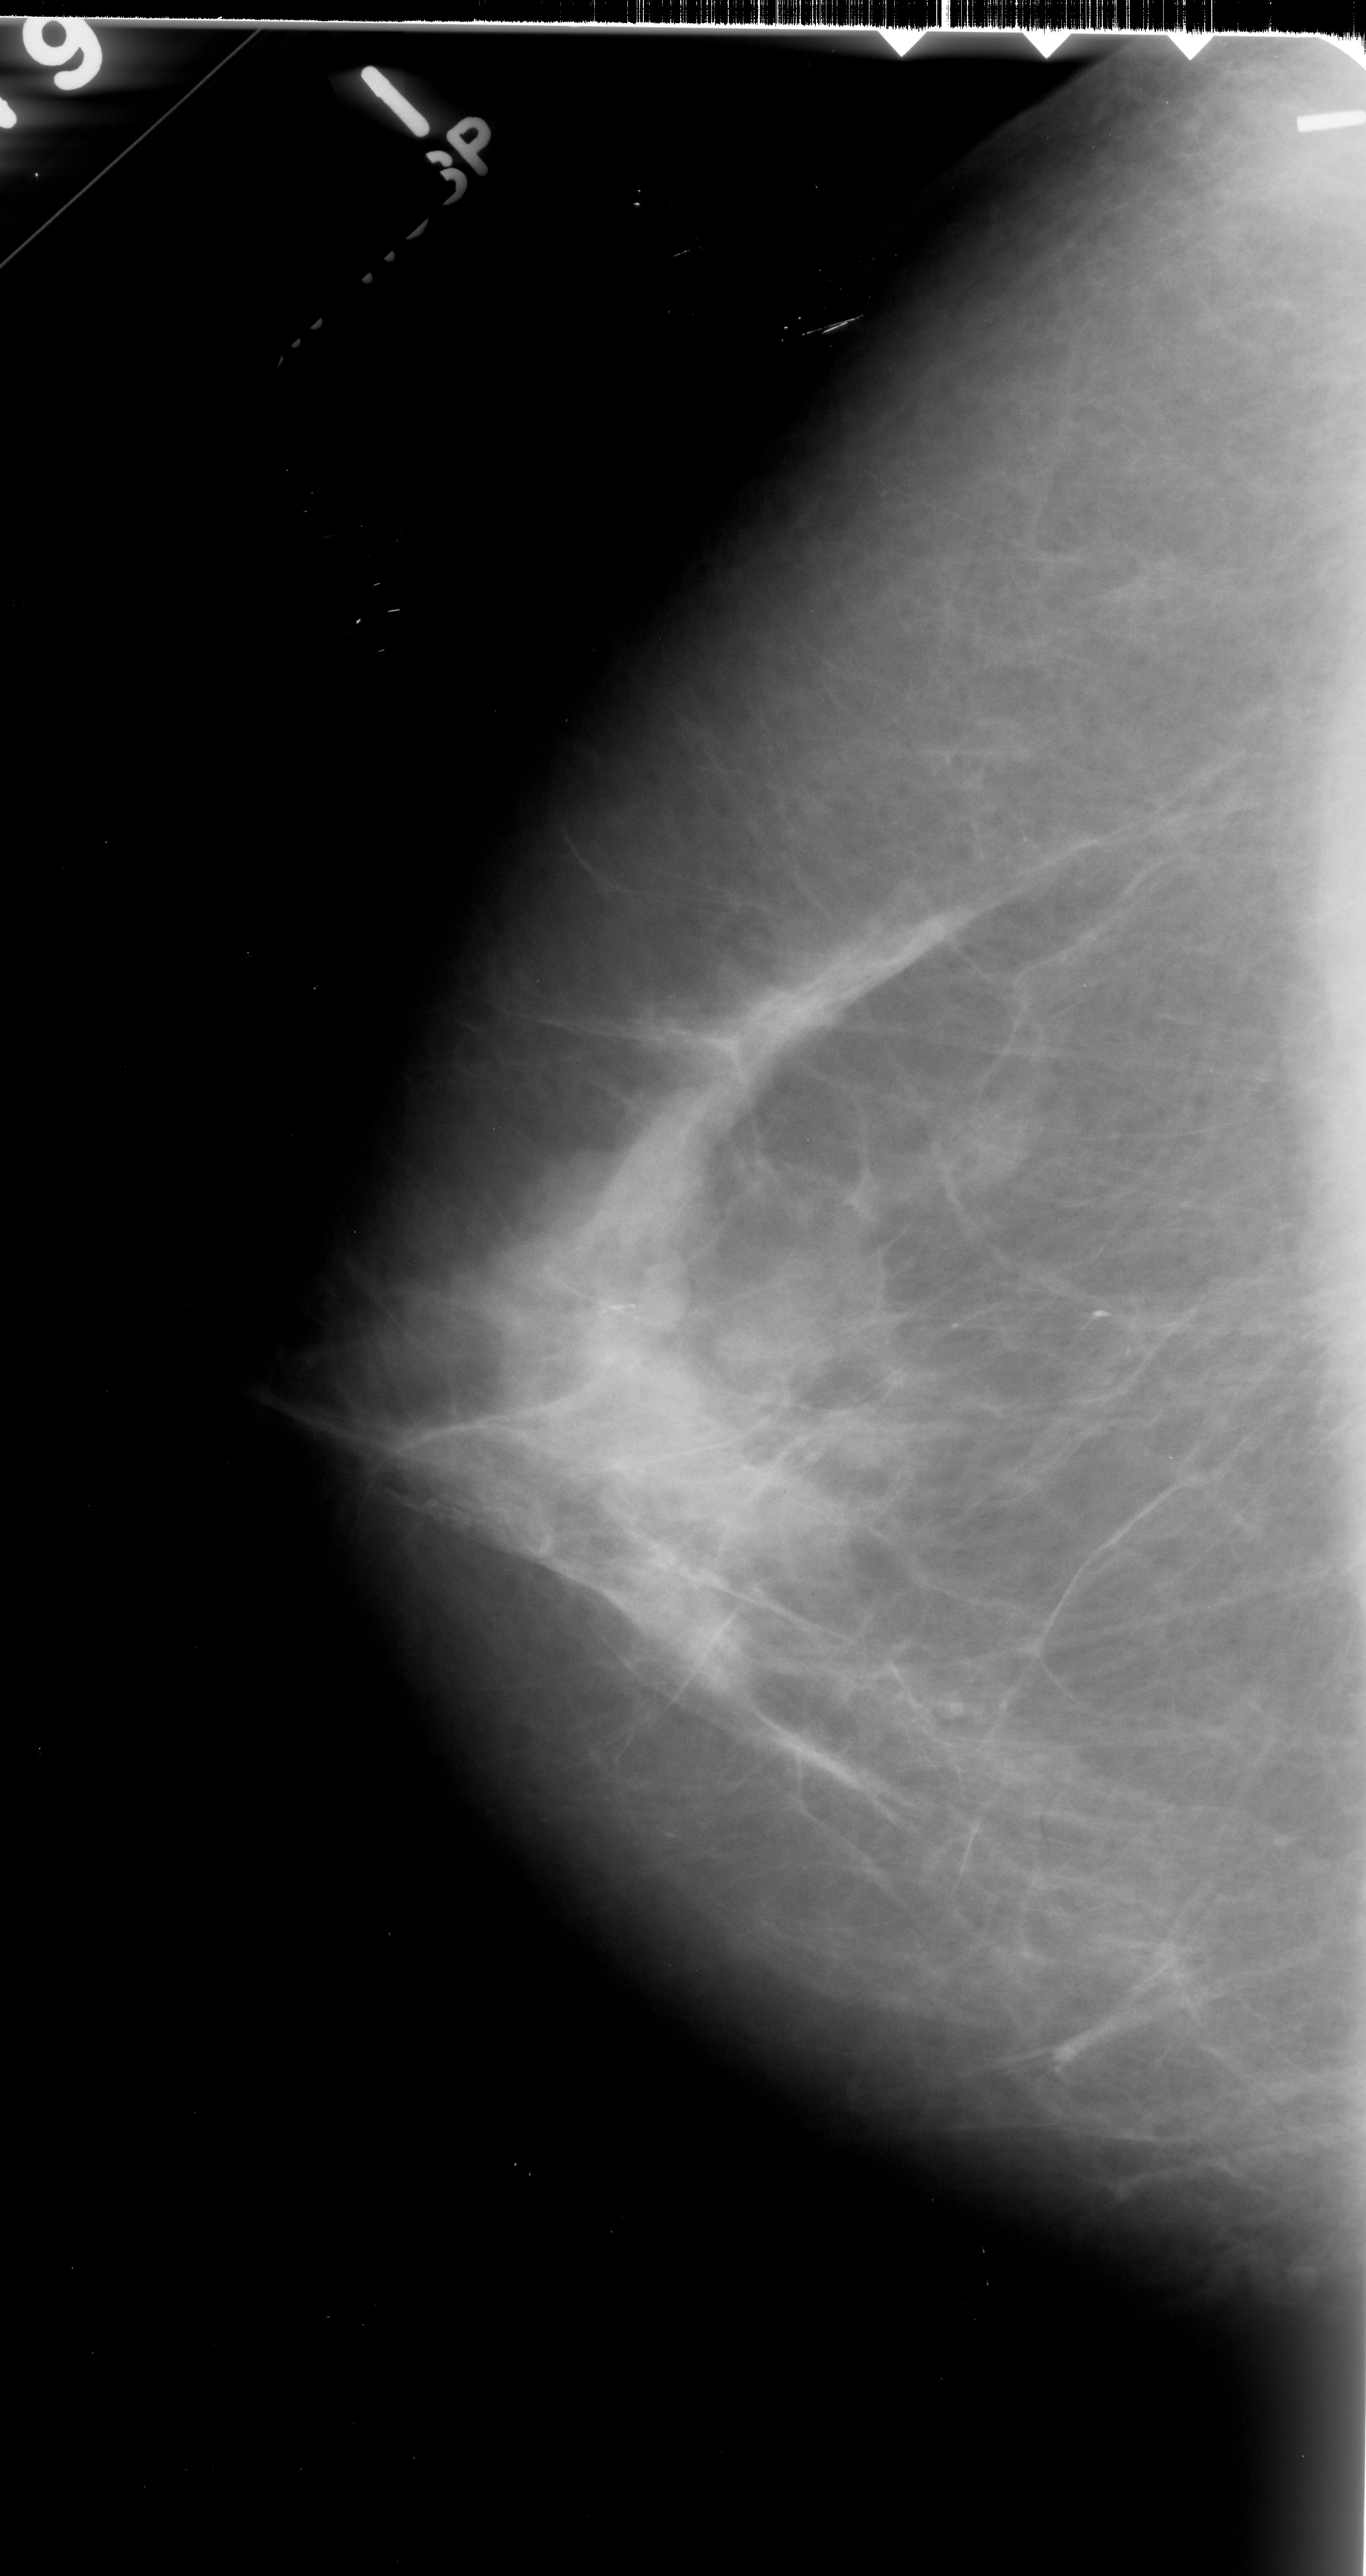
Mammogram (digitized film); left breast; CC view; breast composition: scattered fibroglandular densities (BI-RADS density category 2 of 4); 1366 × 2576 image matrix.
Expert-marked regions of interest on this film, with their recorded descriptors:
- calcifications, morphology fine linear branching, distribution linear; BI-RADS assessment category 4; pathology (as recorded): malignant: bounding box (x1, y1, x2, y2) in pixels: (581, 1288, 653, 1337)